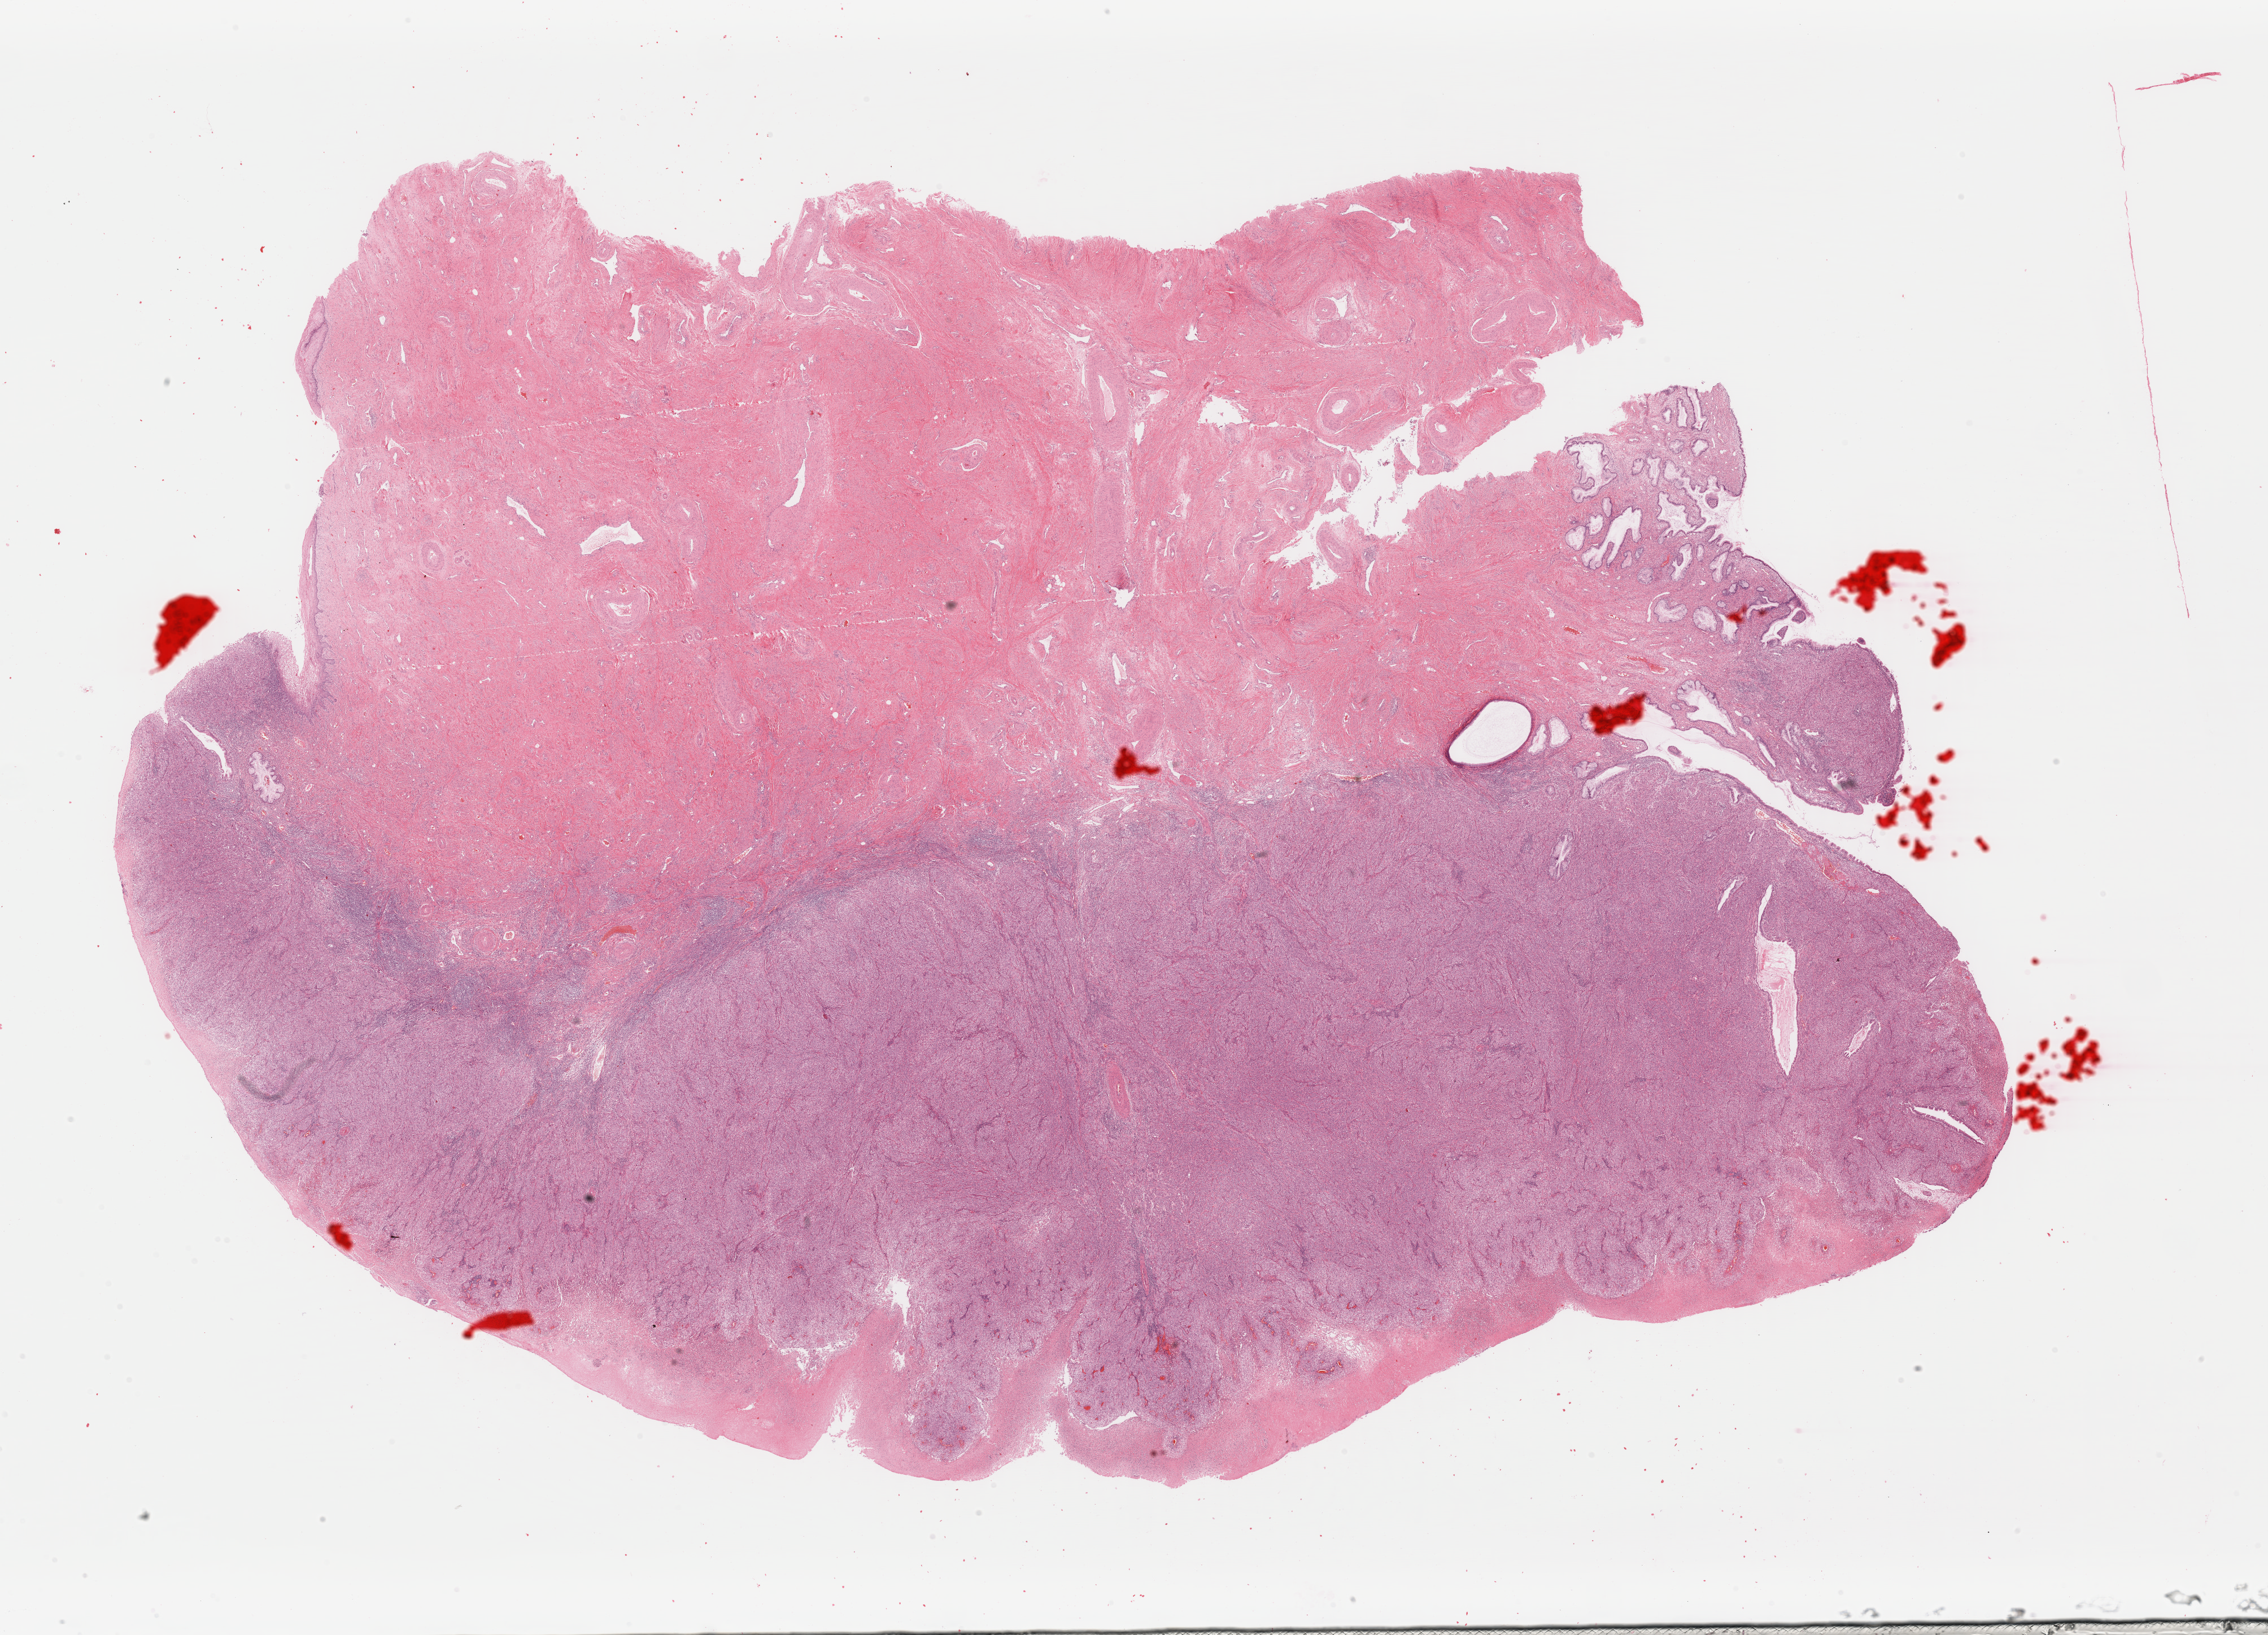
Digitized Hematoxylin and eosin (H&E) stained tissue section (whole slide), a low-resolution overview of the entire scanned area, about 31.7 x 22.8 mm (slide scanned at 40x), formalin-fixed paraffin-embedded (FFPE) diagnostic section, primary tumour sample from the cervix. Female, age 40 years at initial diagnosis. Histologic grade: G3 (poorly differentiated).
FIGO stage: IB. Histologic diagnosis: Squamous cell carcinoma, NOS (cervix uteri).